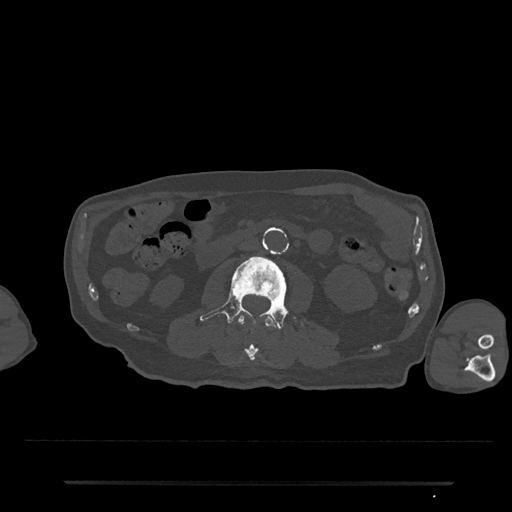
CT including the spine, one axial slice. Position 7 of 797 along the scan axis. Bone window (W 1800 / L 400 HU). 0.5 mm slice thickness. 512 × 512 image matrix, field of view 427 × 427 mm. Male patient, age 74 years. Case-level facts recorded for this patient, not image findings: primary cancer: prostate.
Annotated regions visible in this slice (semi-automatically segmented with operator editing):
- L2 vertebra: box from (x=237, y=314) to (x=278, y=361) px
- L3 vertebra: (x=200, y=256)–(x=305, y=329)